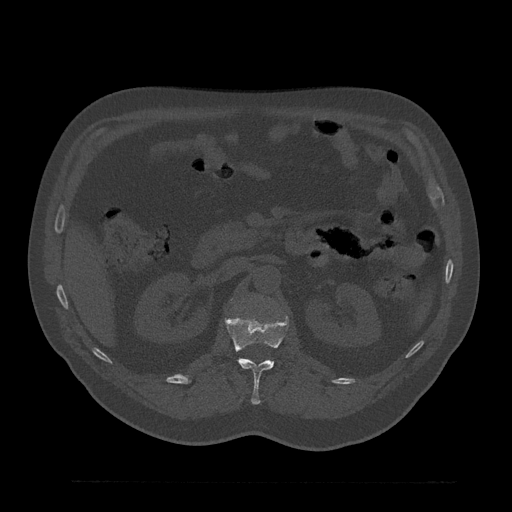
CT including the spine, one axial slice. Slice 155 of 797 in the series (ordered by position). Reconstruction kernel Br40s/3. 120 kVp. Bone window (W 1800 / L 400 HU). 0.5 mm slice thickness. 512 × 512 image matrix. Male patient, age 61 years. From the clinical record (not read from this slice): primary cancer: prostate.
Outlined on this slice (semi-automatic segmentation, software-assisted and operator-edited):
- L1 vertebra: bounding box [x1, y1, x2, y2] px = [211, 315, 289, 405]